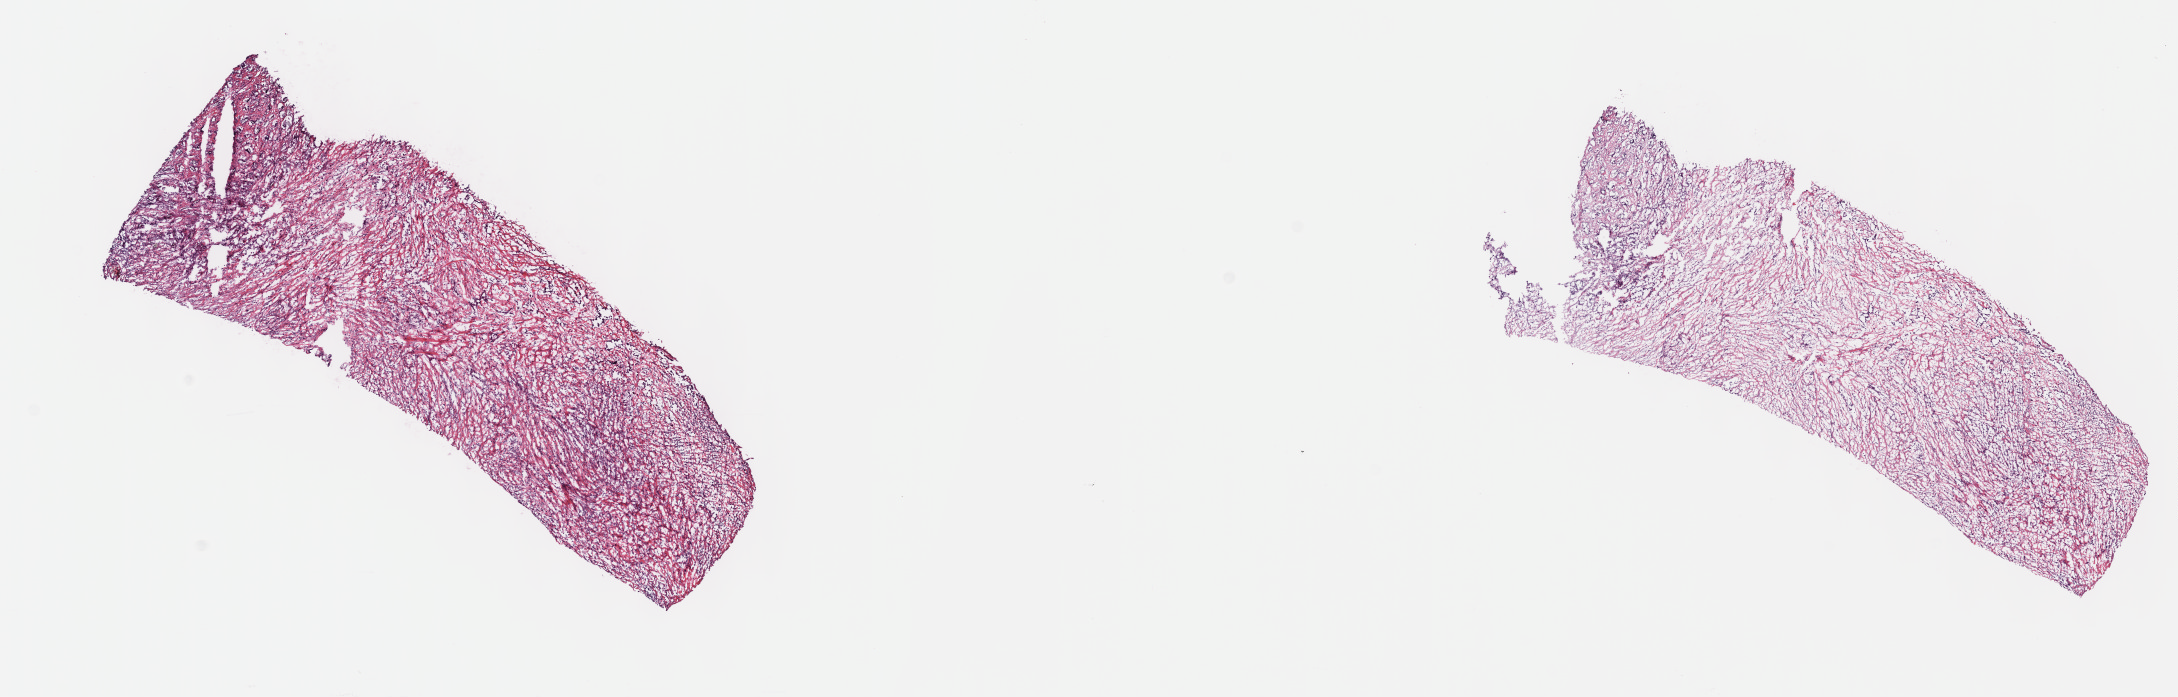
H&E-stained whole-slide image — low-resolution overview of the scanned area, about 17.6 x 5.6 mm; frozen section from the top of the tissue portion; sample: primary tumour, mesothelium. Patient: male, age at initial diagnosis 62 years. Pathologist review of this section (percent, as recorded): tumour cells 100%, tumour nuclei 80%, normal cells 0%, stromal cells 0%, necrosis 0%. Infiltration values recorded for this section: lymphocyte infiltration 0%, monocyte infiltration 0%, neutrophil infiltration 0%.
AJCC pathologic stage: III. Histologic diagnosis: Mesothelioma, biphasic, malignant (pleura, NOS). Laterality: left.